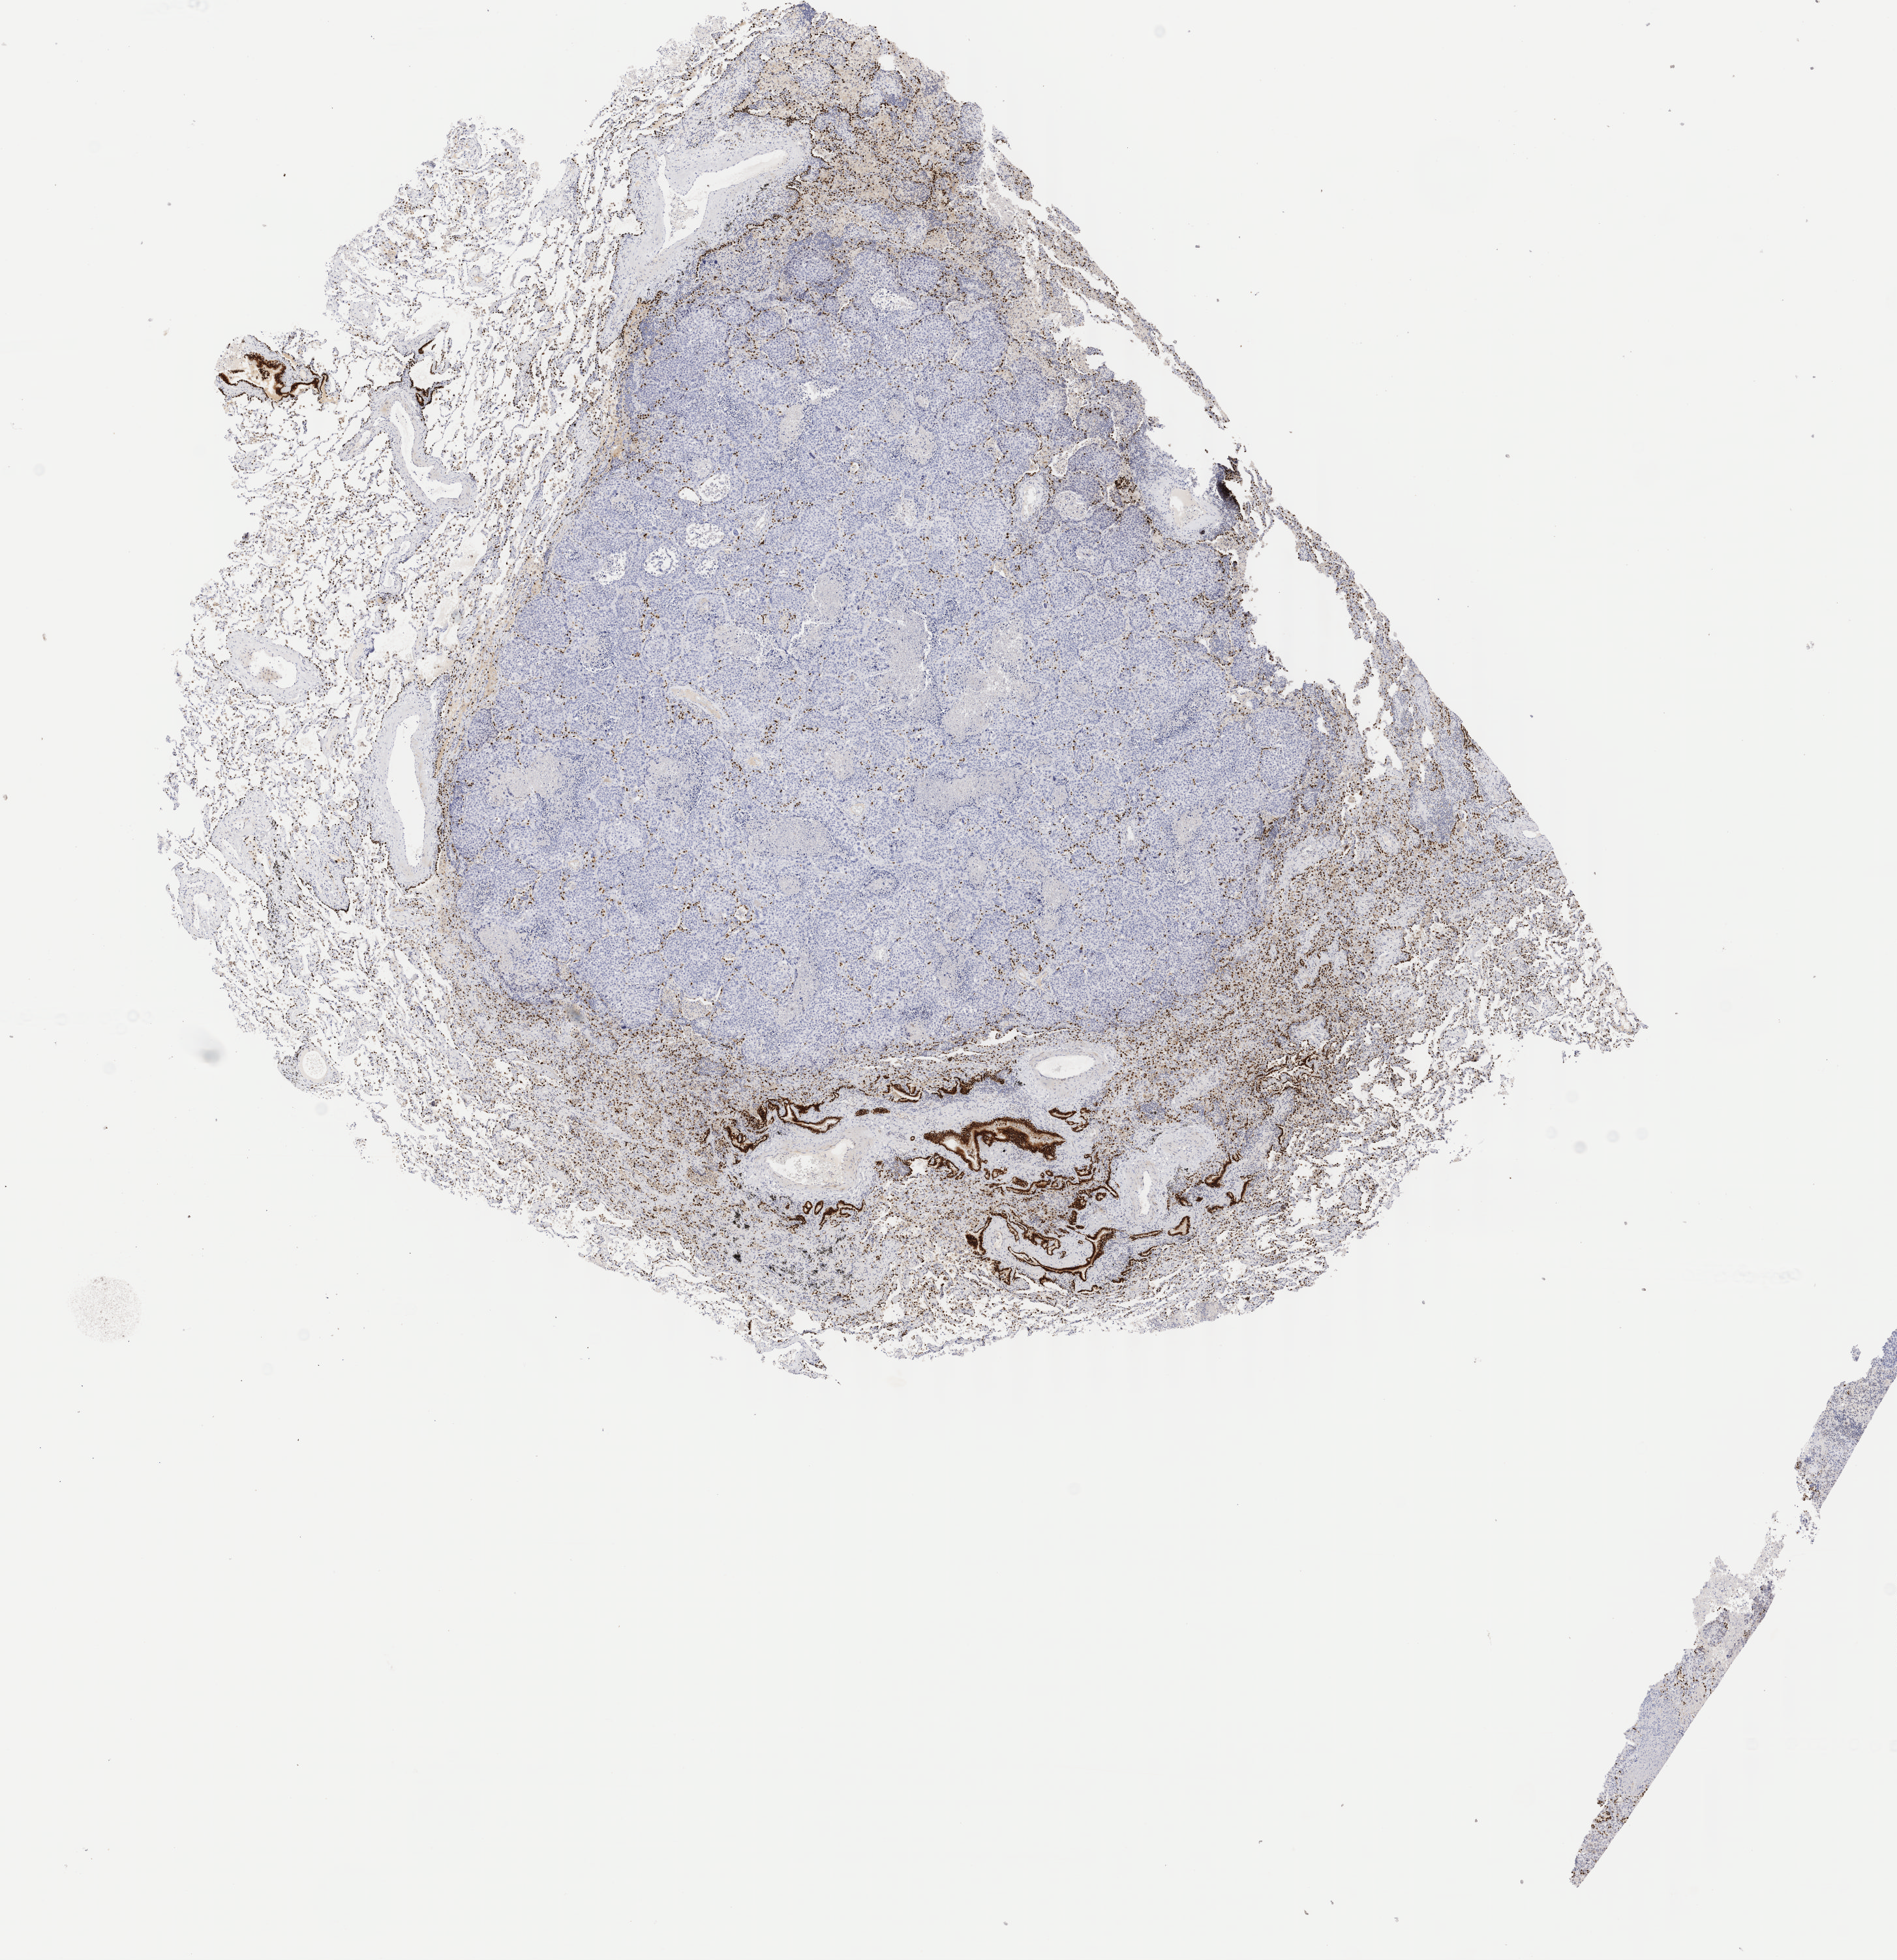
Immunohistochemistry (IHC) whole-slide image stained for TTF-1 (thyroid transcription factor 1) — a low-resolution overview of the entire scanned area, about 11.6 x 11.9 mm; tumor tissue; site: lung (left). Patient: male, aged 66.
Diagnosis: Squamous cell carcinoma, NOS.